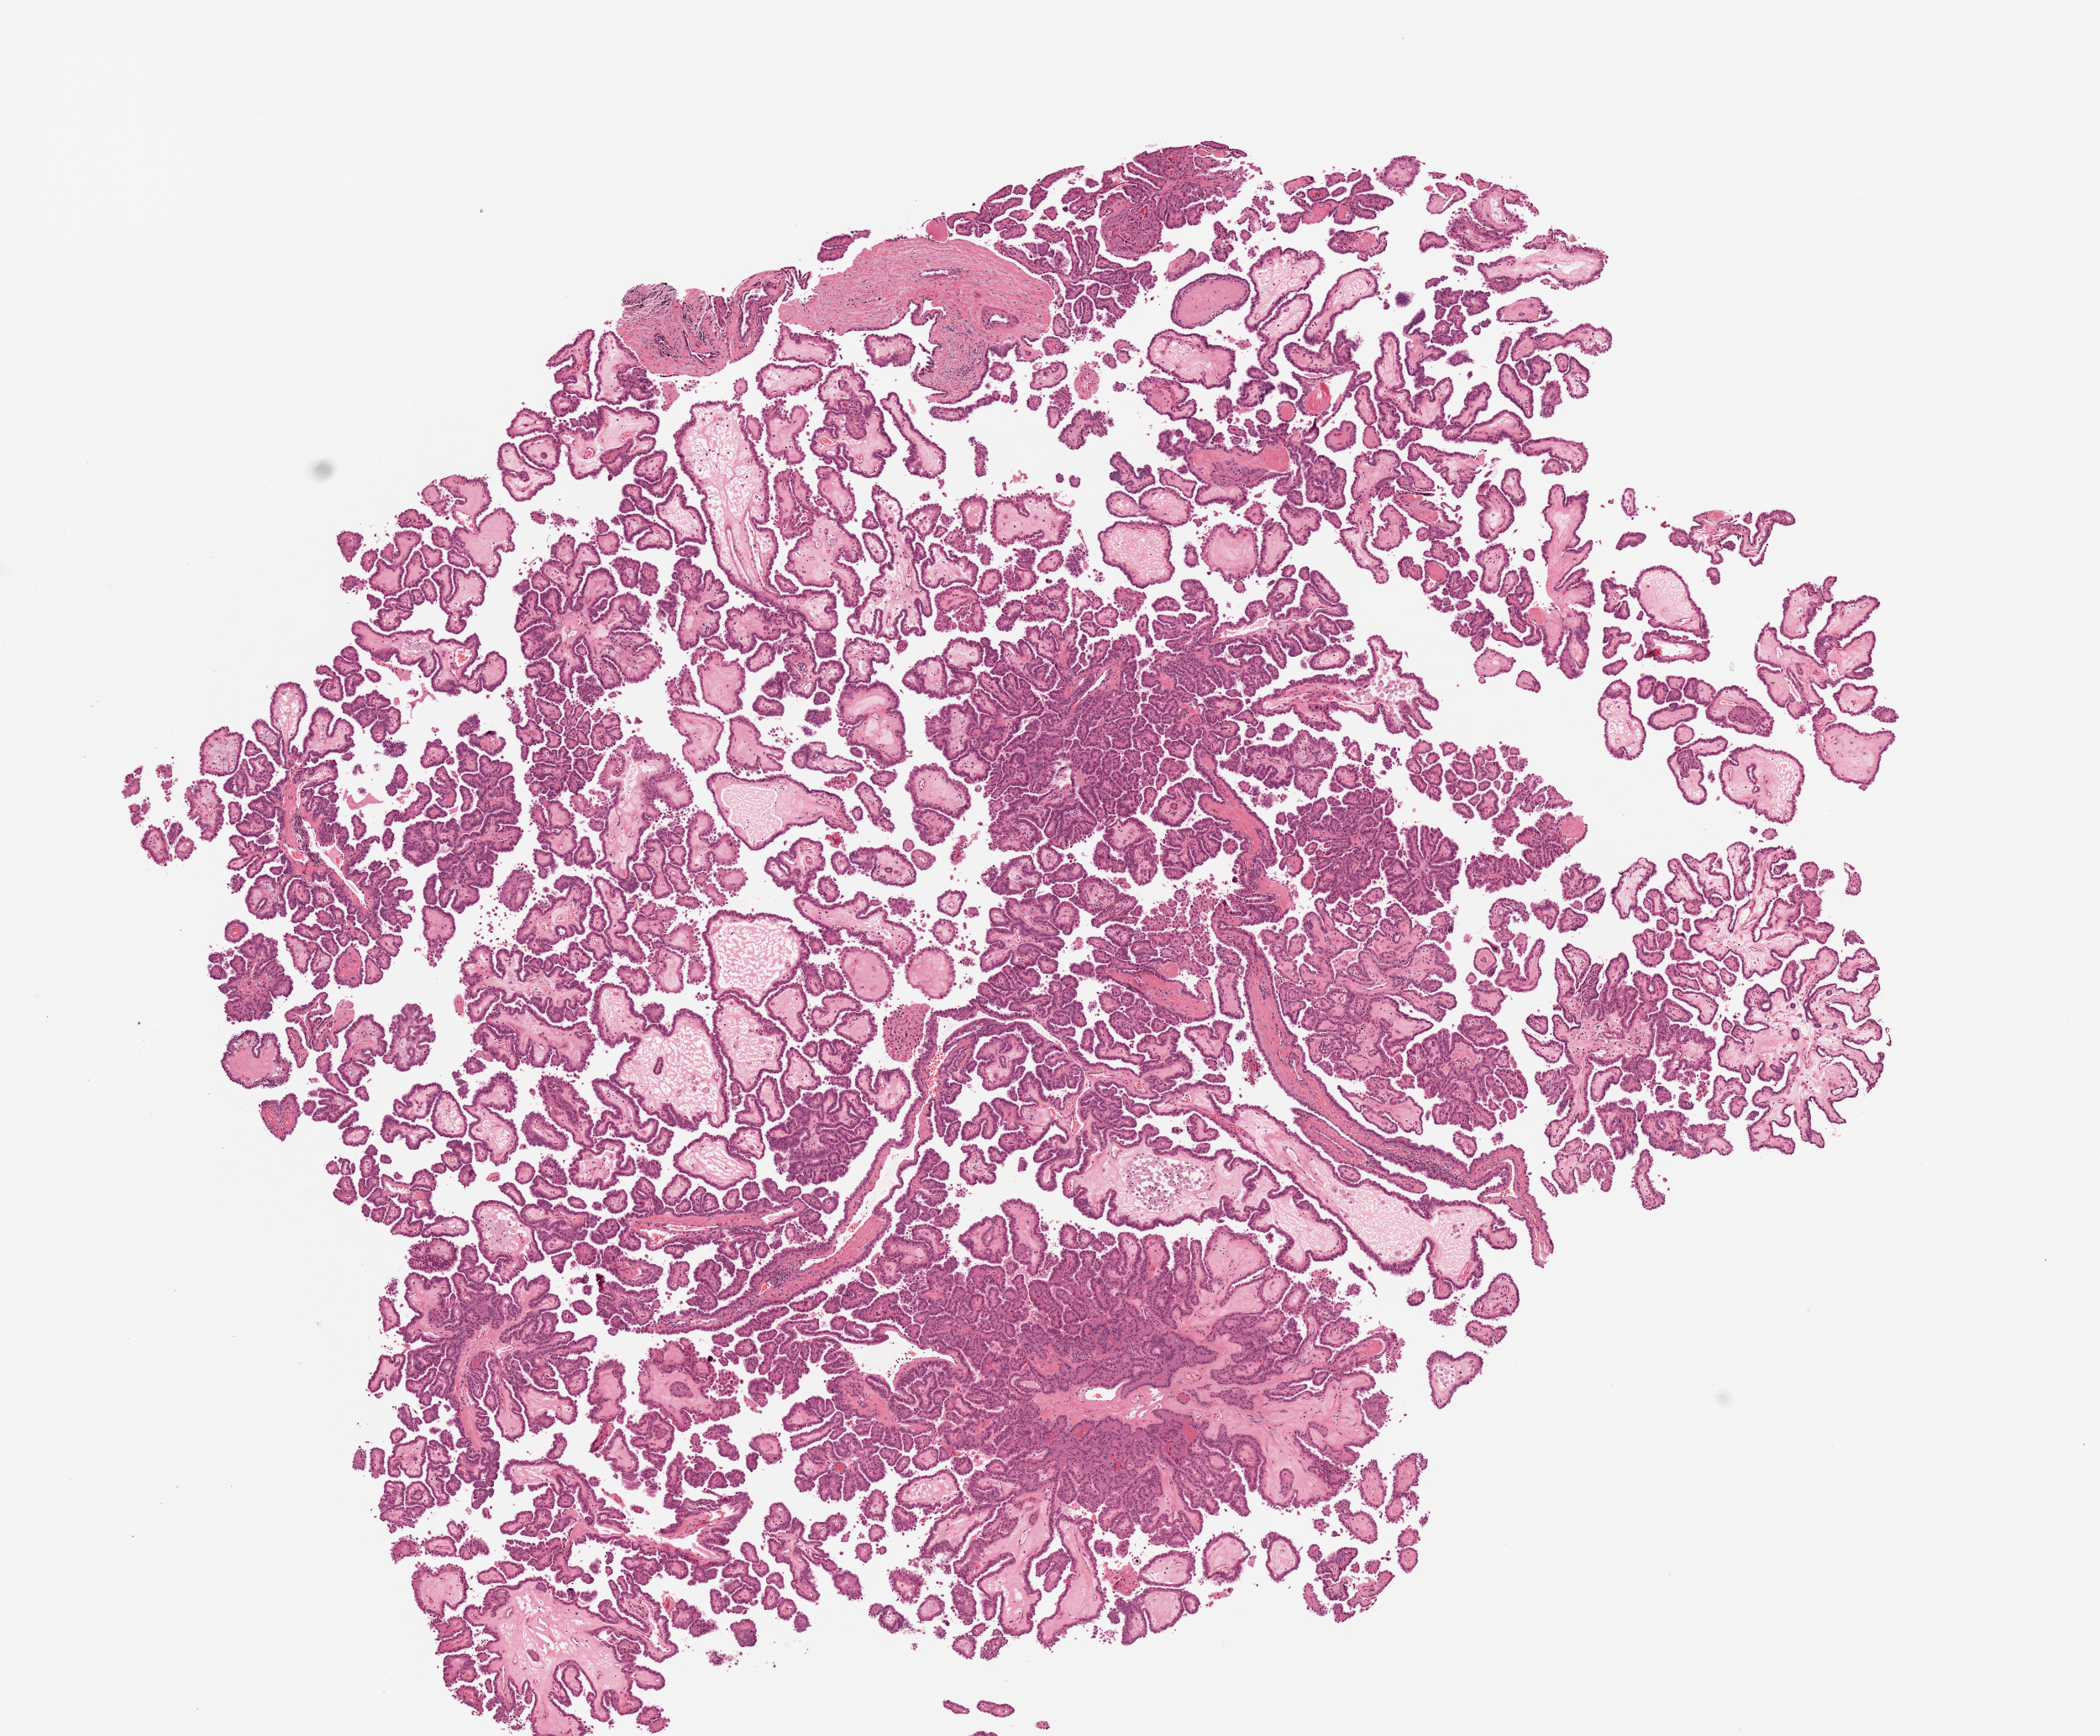
Hematoxylin and eosin (H&E) stained whole-slide image, whole scanned area (about 10.0 x 8.3 mm, from a 20x scan) shown as a low-resolution overview. FFPE section. Thyroid, primary tumour sample. Patient: female, age at initial diagnosis 28 years.
AJCC pathologic stage: I (7th edition). Lymph nodes positive (case pathology): 3 of 4 examined. Diagnosis: Papillary adenocarcinoma, NOS. TNM: T3 N1a MX.